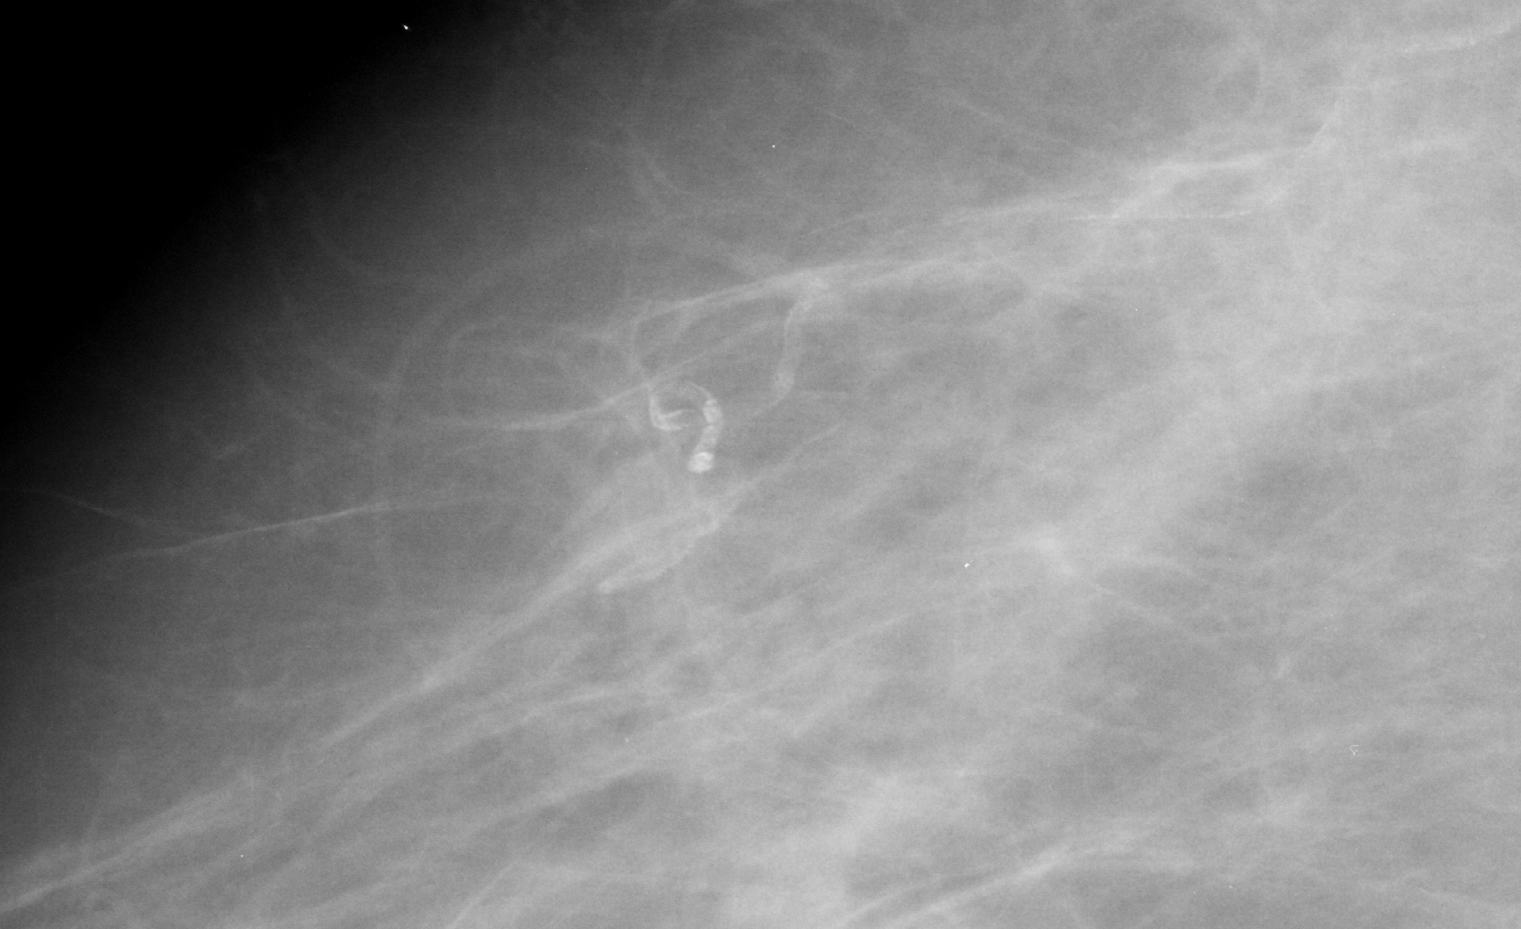
Region of interest cut from a scanned film mammogram (one marked finding), right breast, CC view.
Marked abnormality: calcifications, morphology vascular; BI-RADS assessment category 2; subtlety rating 3 on a 1 (subtle) to 5 (obvious) scale; benign without callback (not worked up further).